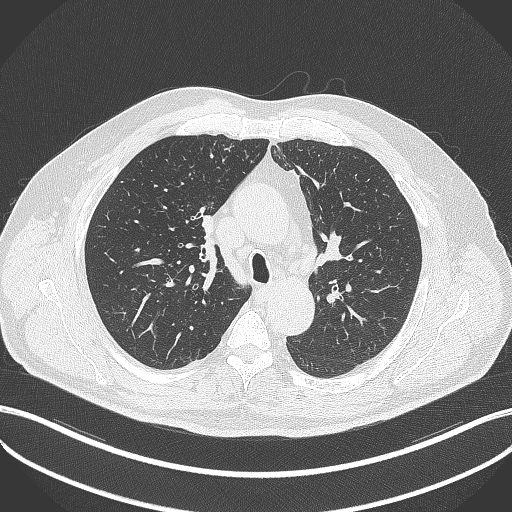
Chest CT, one axial slice. Position 260 of 411 along the scan axis. Reconstruction kernel B70f. 120 kVp. Lung window (W 1500 / L -600 HU). 512 × 512 image matrix, field of view 400 × 400 mm. Patient: male, 60 years. Case-level facts recorded for this patient, not image findings: clinical TNM (as recorded): T1b N1 M0.
Annotated regions visible in this slice (rectangle marked by the reading radiologist):
- lung tumour (recorded histology: squamous cell carcinoma): box from (x=201, y=213) to (x=216, y=240) px